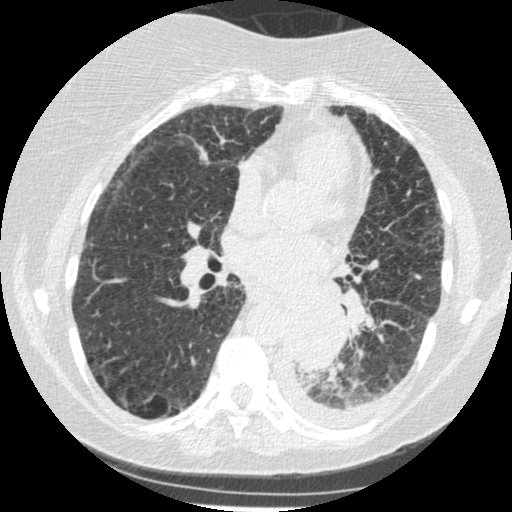
Low-dose screening chest CT, one axial slice; slice 118 of 341 in the series (ordered by position); reconstruction kernel STANDARD; 120 kVp; lung window (W 1500 / L -600 HU); 512 × 512 image matrix.
Outlined on this slice (outlined manually by an expert reader):
- lesion 1 (tumor, lower lobe of left lung): bounding box <283,301,344,369> (left, top, right, bottom; pixels)